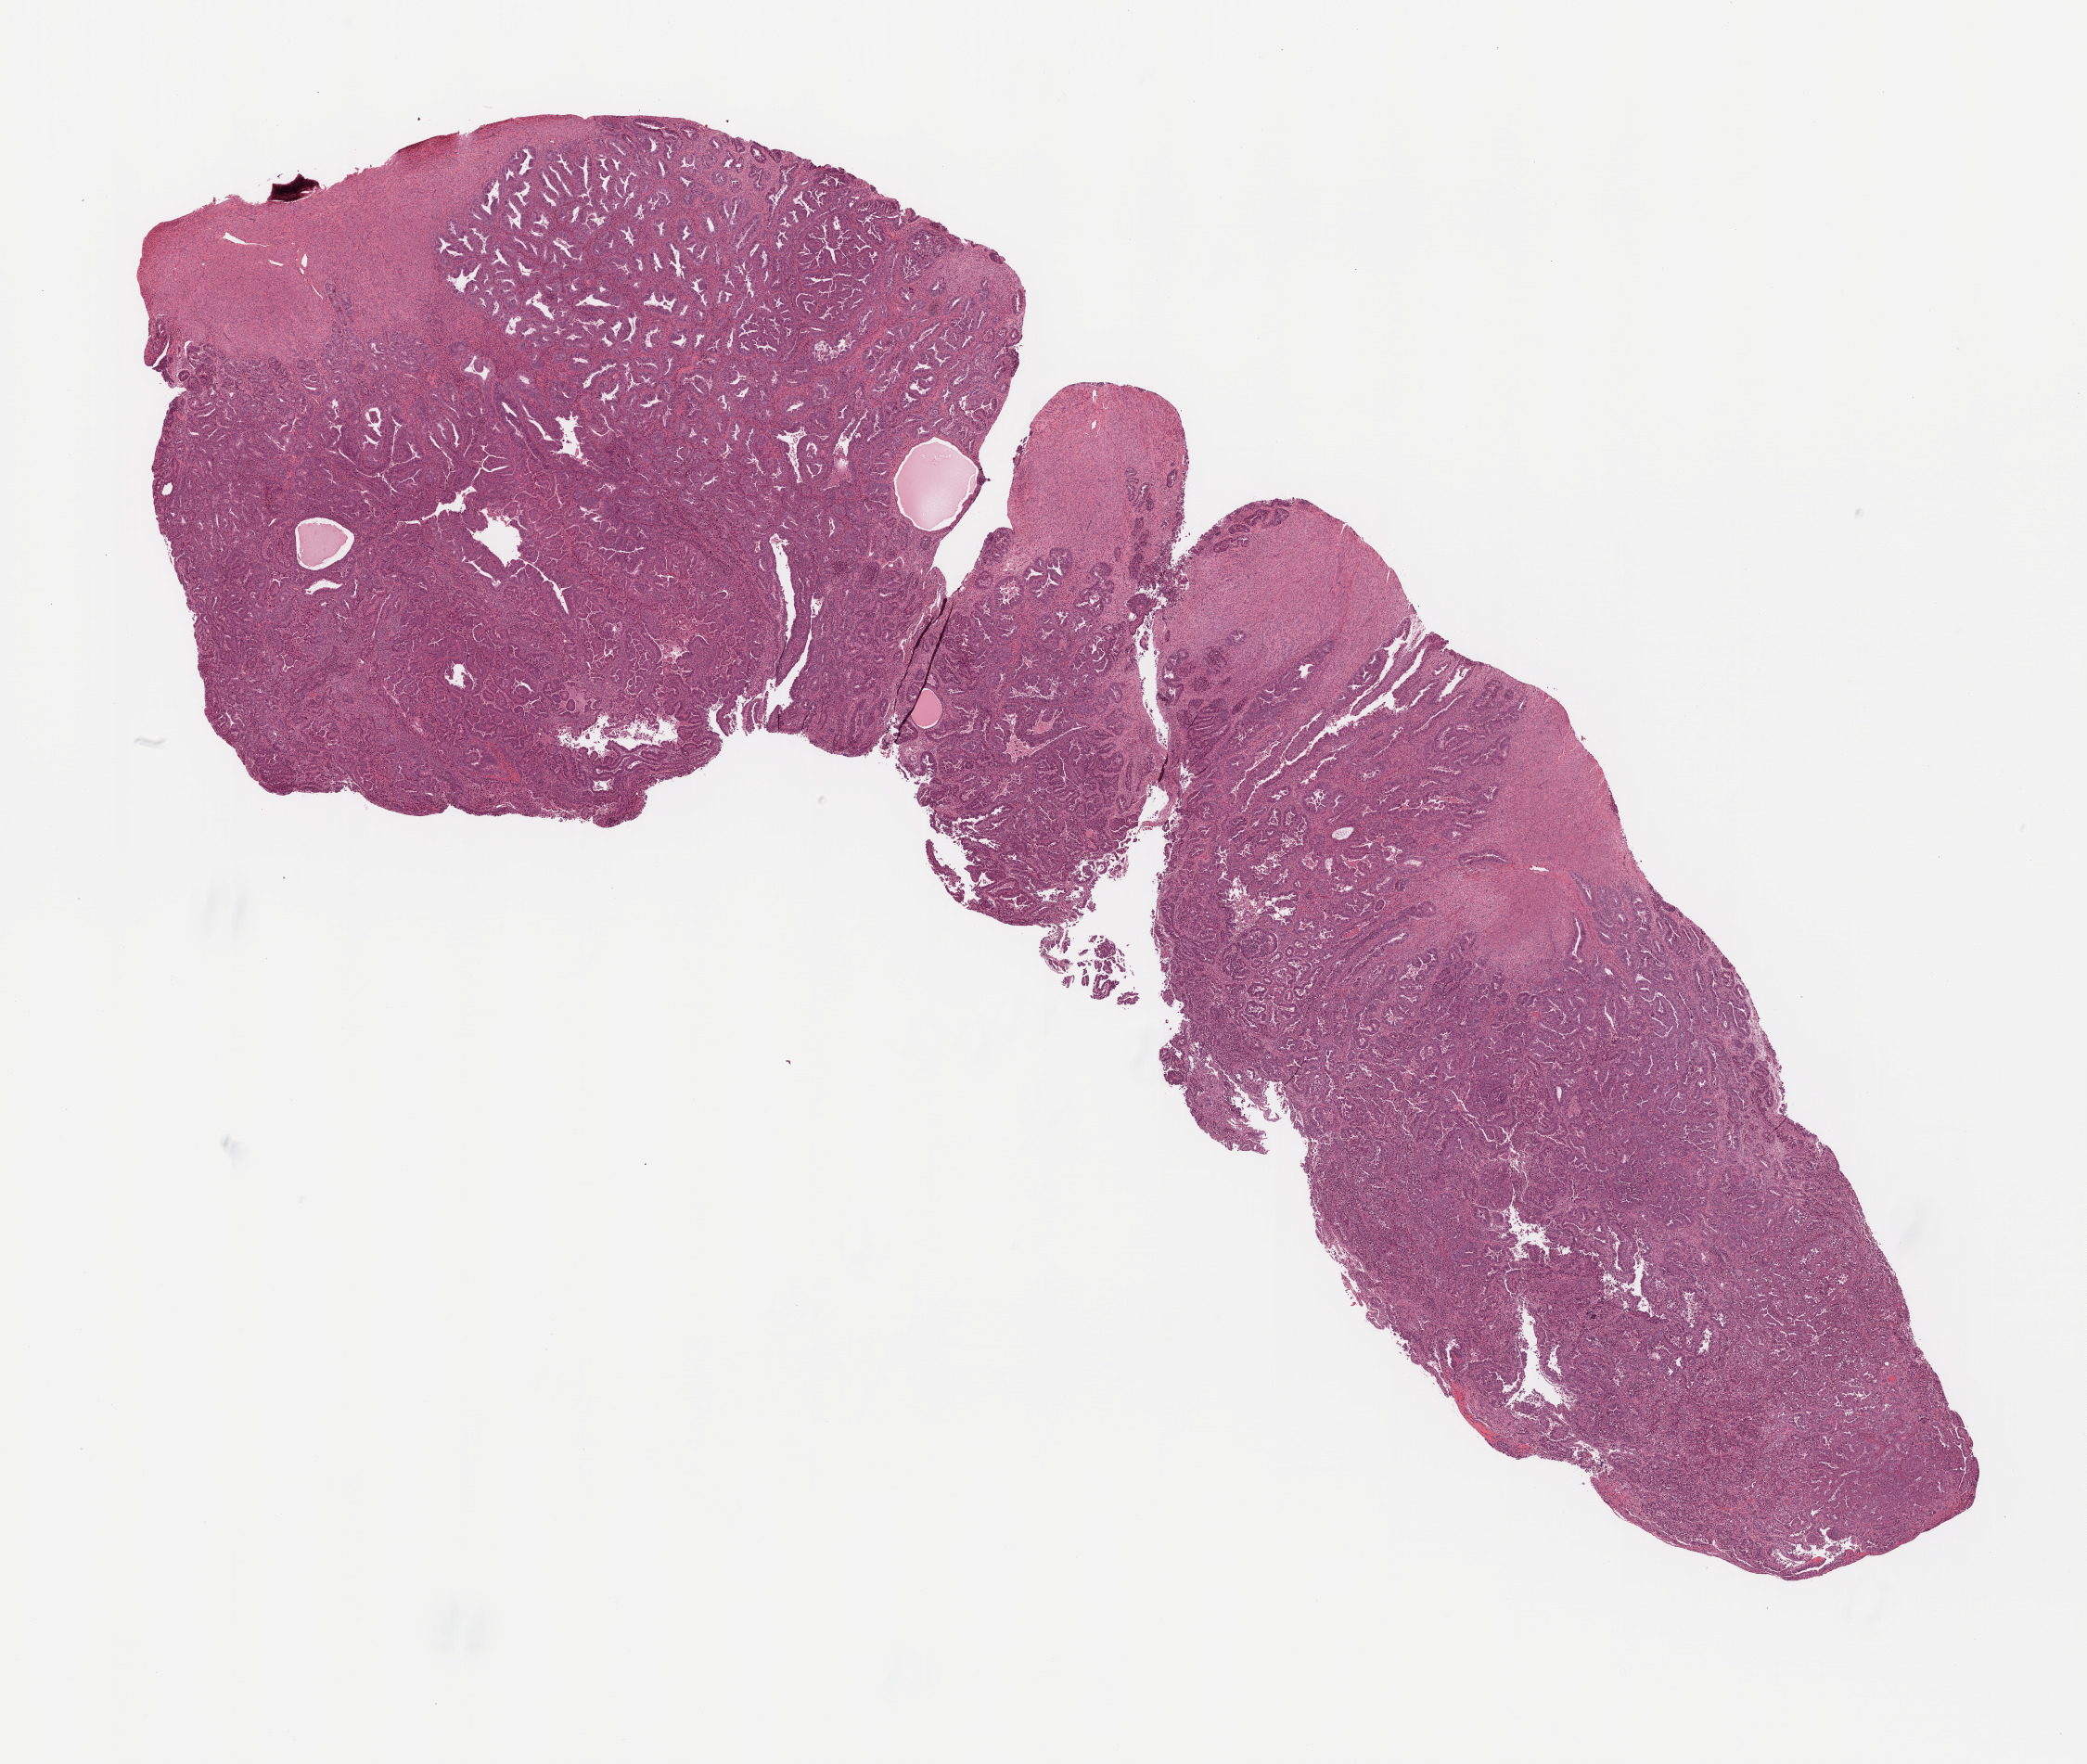
H&E-stained whole-slide image, shown as a low-resolution overview of the whole scanned area (about 18.1 x 15.3 mm, acquisition: 20x scan). FFPE section. Uterus, primary tumour sample. Patient: female, age at initial diagnosis 69 years. Histologic grade: G3 (poorly differentiated).
Histologic diagnosis: Serous cystadenocarcinoma, NOS (endometrium). FIGO stage: IA. Lymph nodes positive (case pathology): 0 of 11 examined.